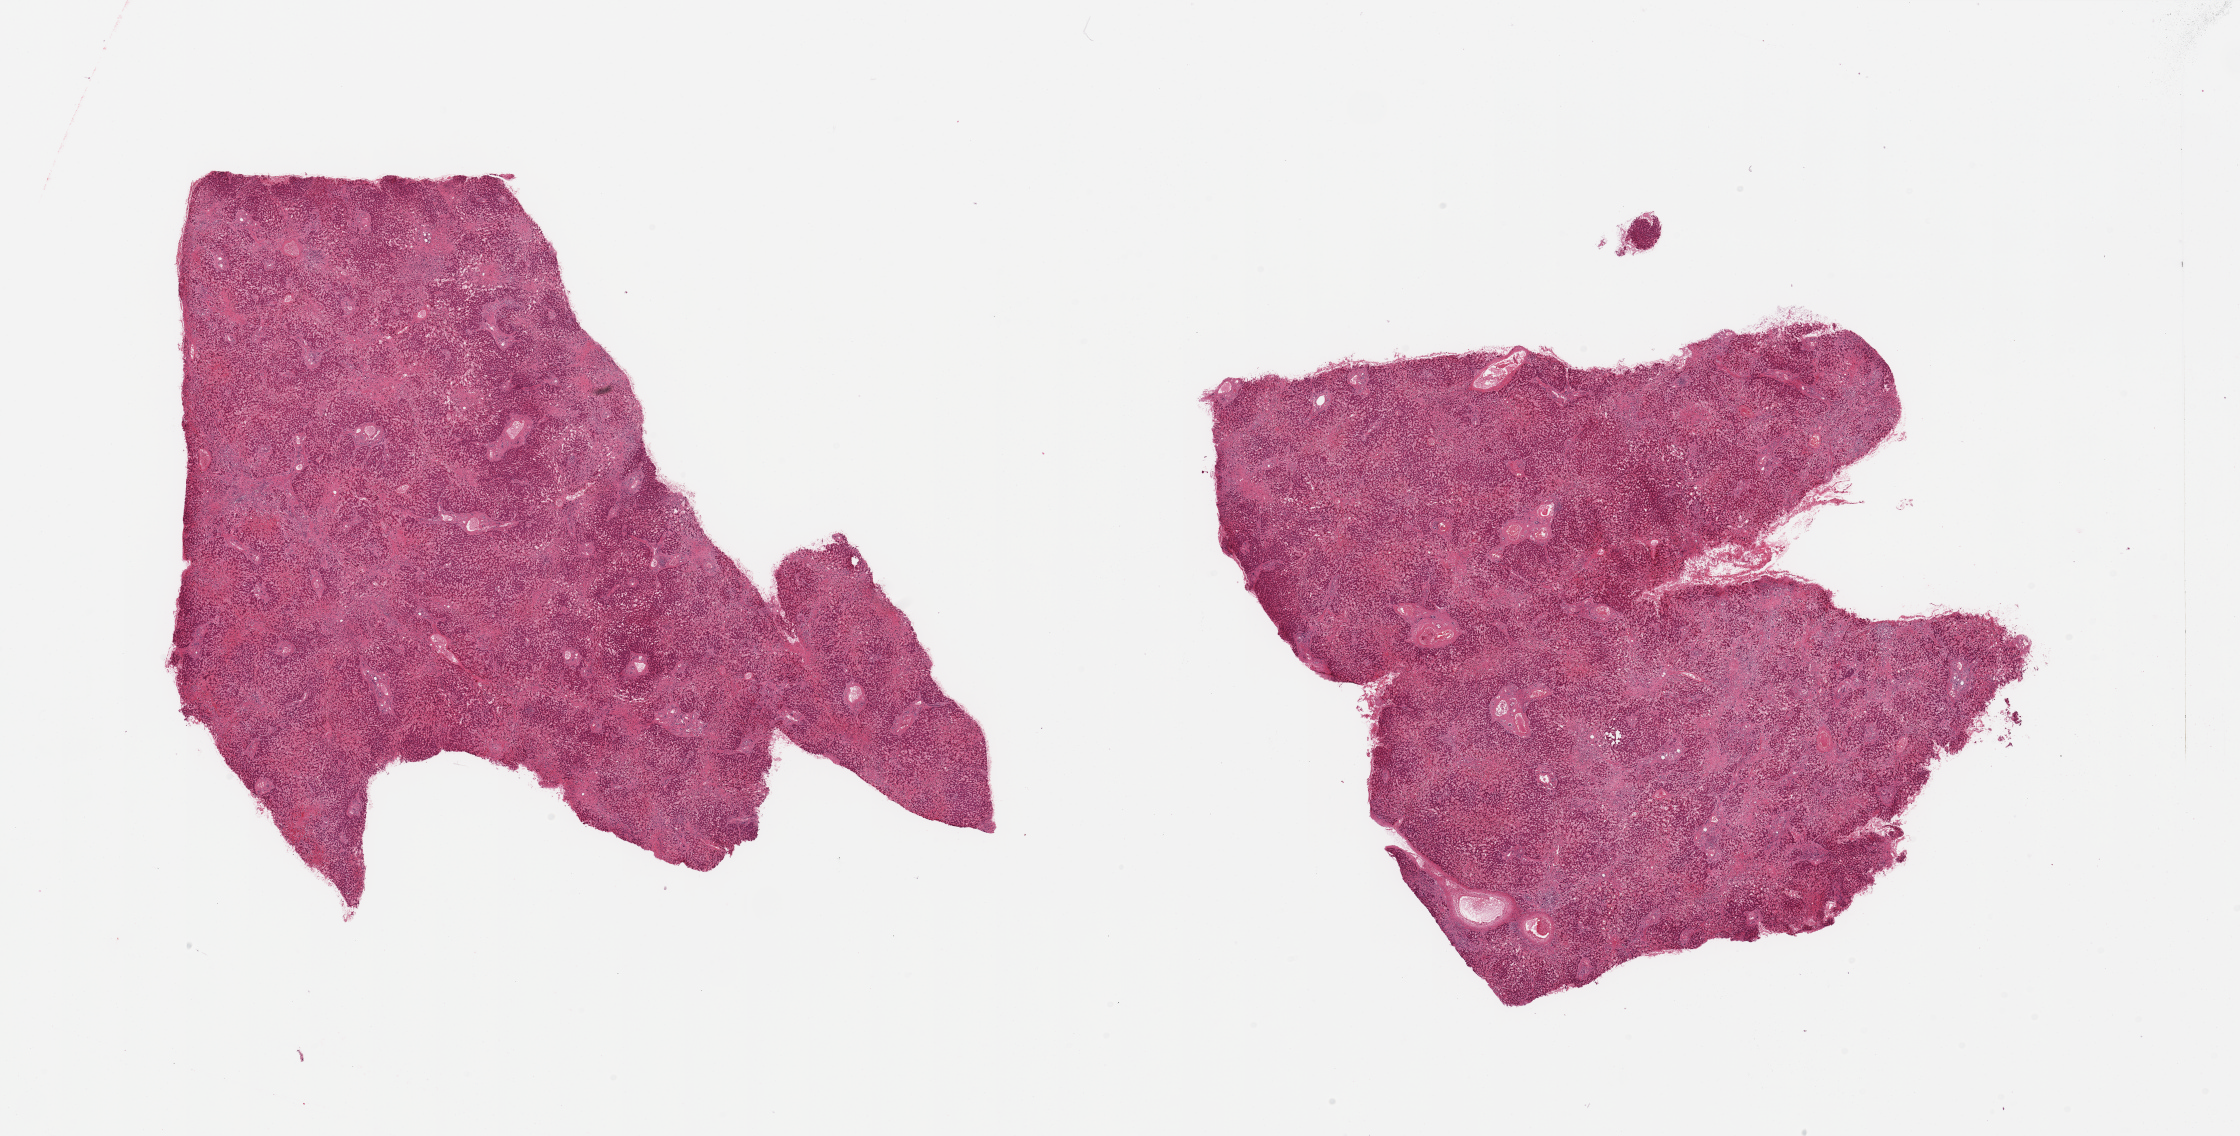
Whole-slide image, haematoxylin and eosin stain — a low-resolution overview of the entire scanned area, about 35.4 x 18.0 mm, PAXgene-fixed paraffin-embedded (PFPE) section, section of liver (target tissue), donor tissue sample. Donor: male.
Reviewer comment on this tissue sample: 2 pieces; congestion and cardiac sclerosis (cirrhosis).